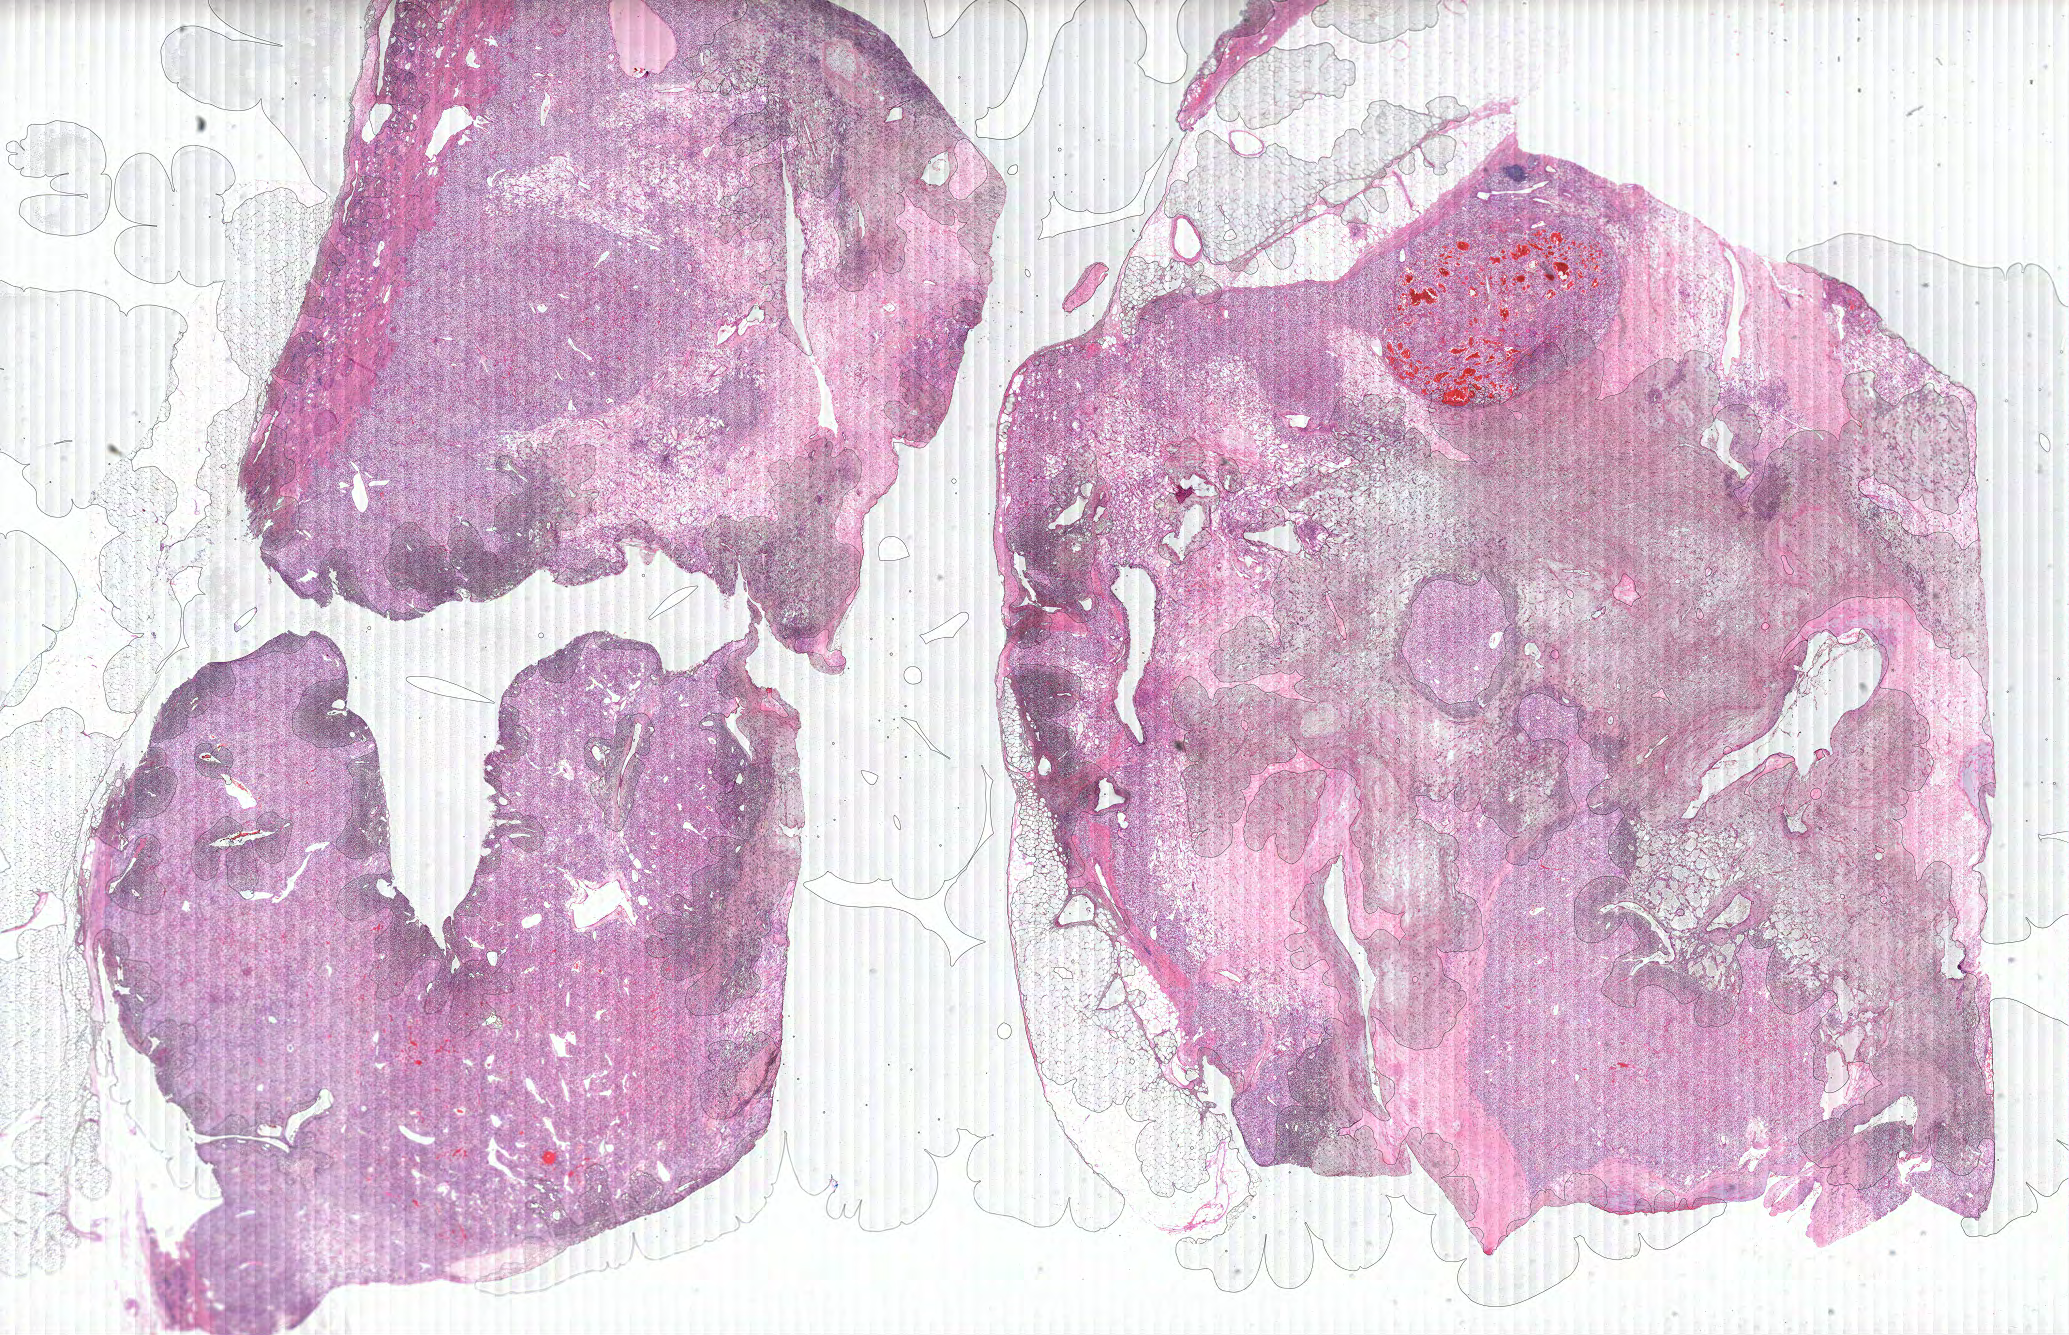
H&E-stained whole-slide image — whole scanned area (about 33.1 x 21.3 mm, slide scanned at 40x) shown as a low-resolution overview, formalin-fixed paraffin-embedded (FFPE) diagnostic section, sample: primary tumour, kidney. Male, age 67 years at initial diagnosis. Histologic grade: G2 (moderately differentiated).
- AJCC pathologic stage: III
- pathologic diagnosis: Clear cell adenocarcinoma, NOS